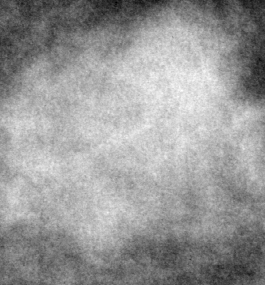
Cropped region of a digitized screen-film mammogram centred on a radiologist-marked abnormality; left breast; MLO view.
Finding: mass, shape lobulated, margins circumscribed / ill defined; BI-RADS assessment category 3; pathology (as recorded): malignant.